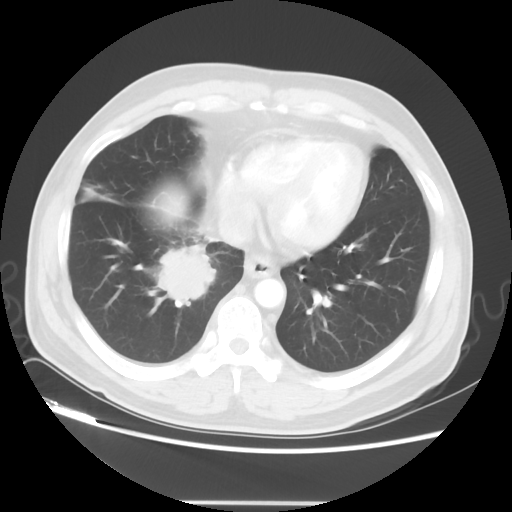
Chest CT, one axial slice. Position 14 of 48 along the scan axis. Lung window (W 1500 / L -600 HU). 512 × 512 image matrix. Male patient, age 53 years. Case-level facts recorded for this patient, not image findings: clinical TNM (as recorded): T2 N3 M0; histopathological grade: G3.
Structures marked on this image (bounding box drawn by a radiologist):
- lung tumour (recorded histology: small cell carcinoma): bounding box (x1, y1, x2, y2) in pixels: (152, 235, 215, 312)